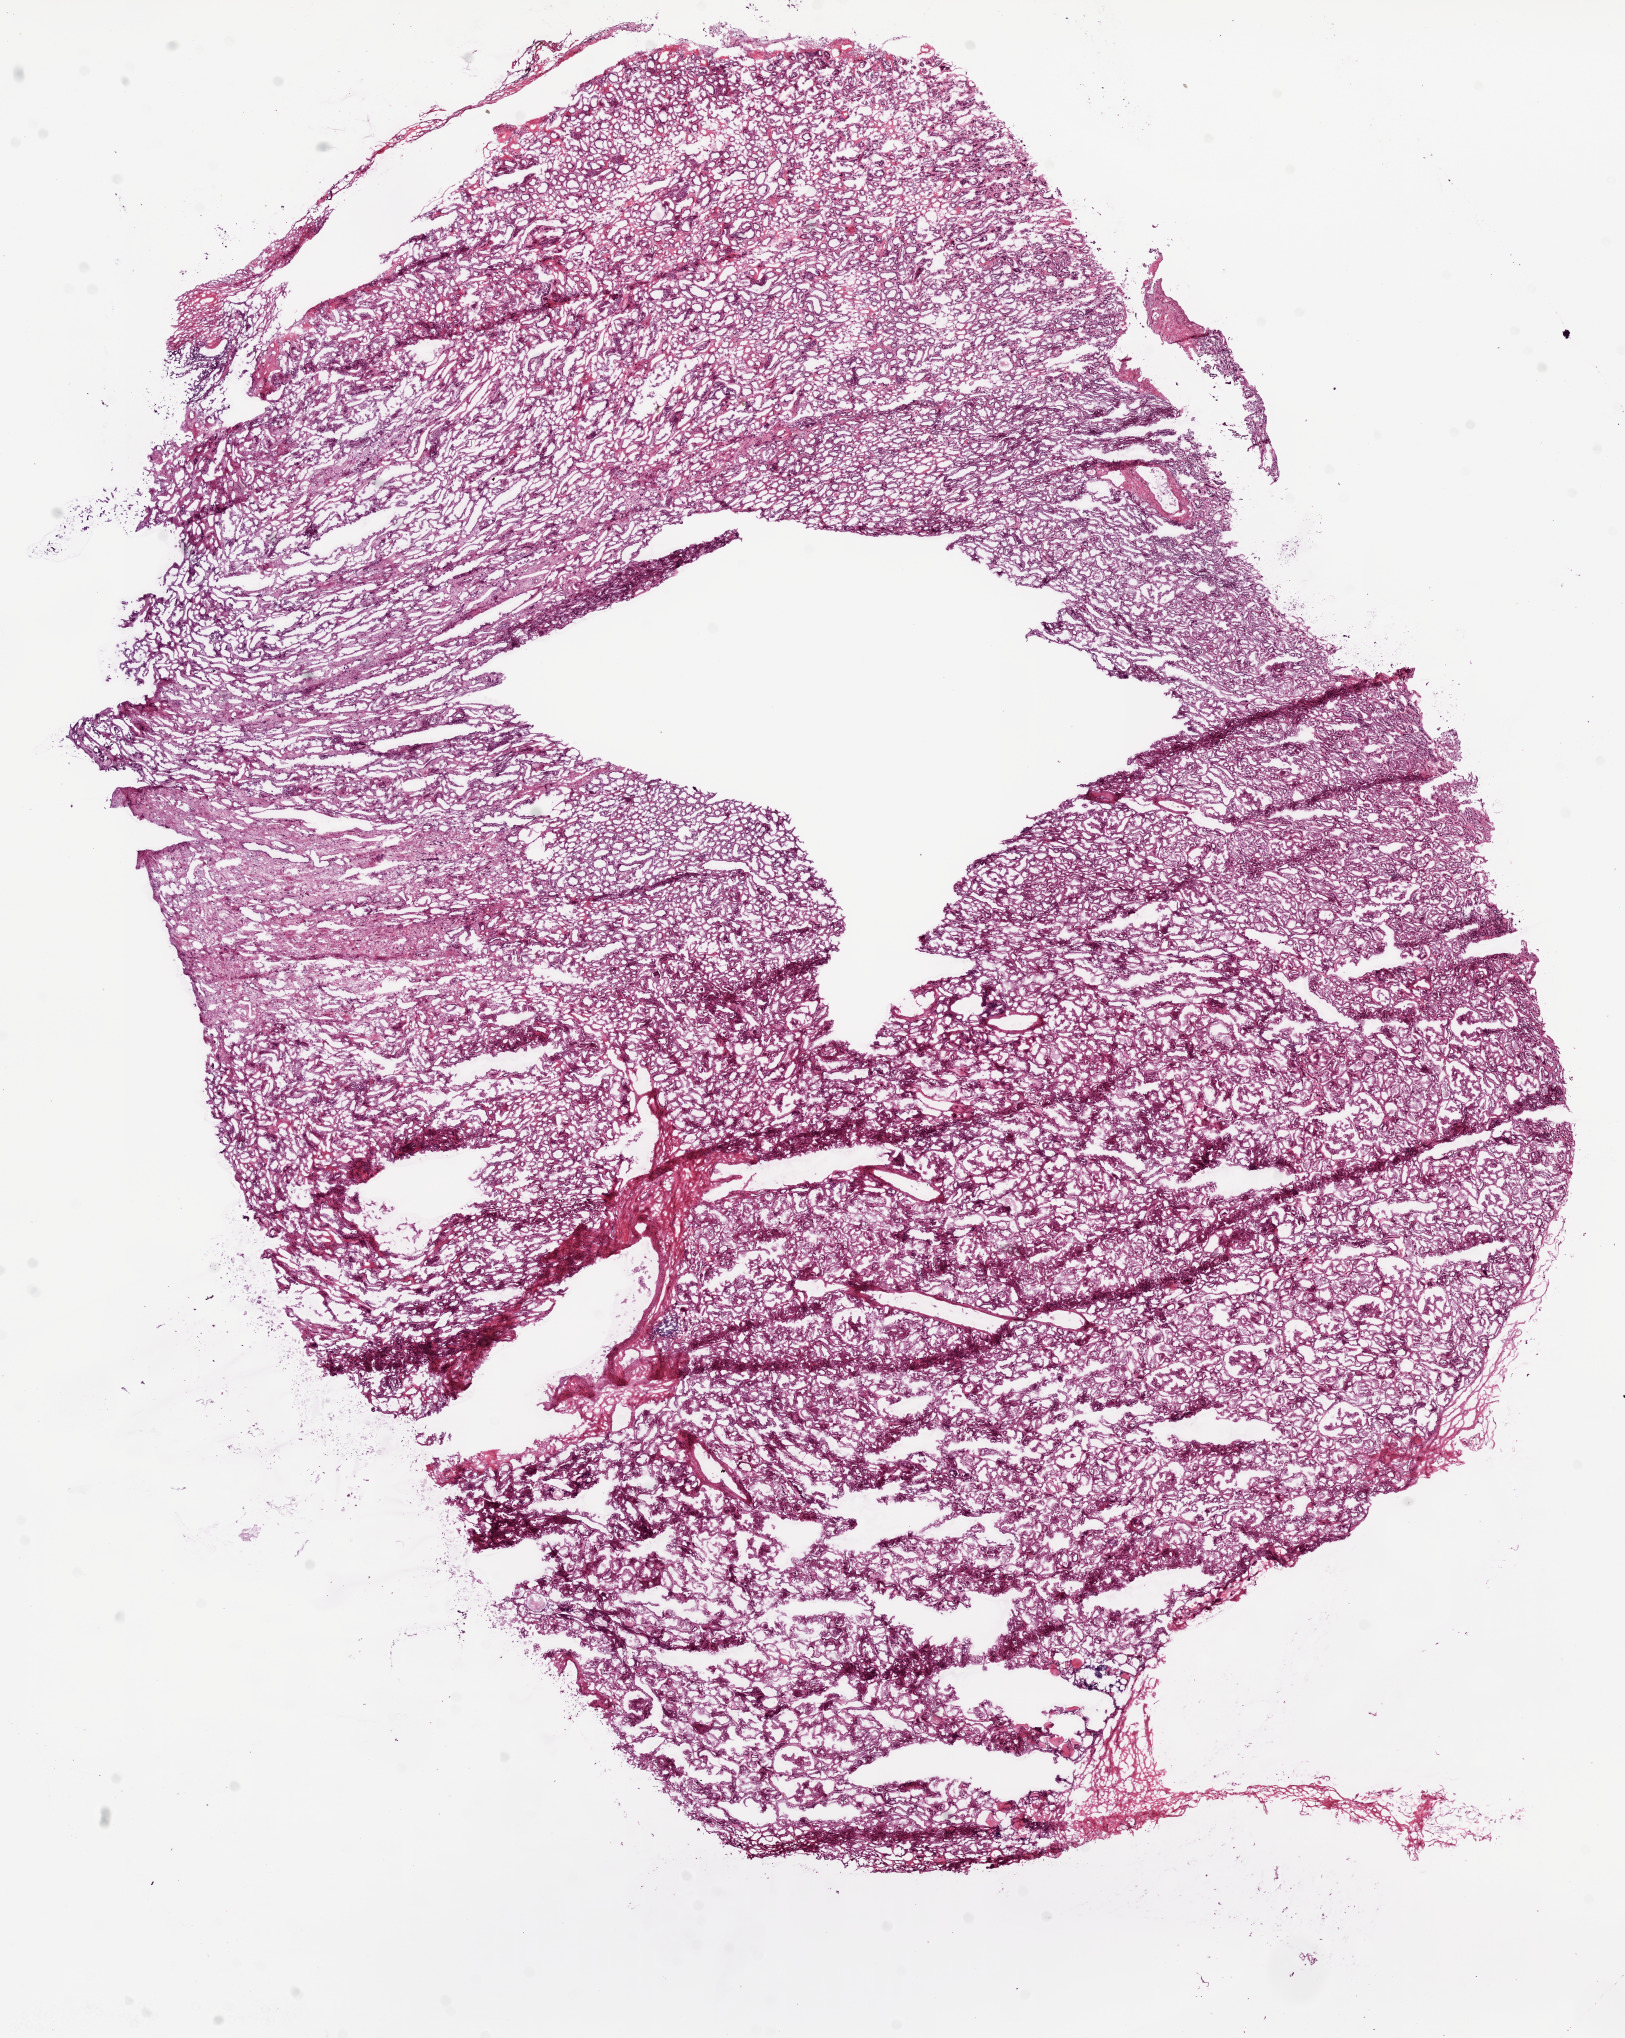
H&E whole-slide image, a low-resolution overview of the entire scanned area, about 13.0 x 16.4 mm (slide scanned at 20x), frozen section, kidney, solid tissue normal (non-tumour tissue) sample. Patient: male, age at initial diagnosis 65 years.
• this section: solid tissue normal sample (biorepository sample class)
• patient diagnosis: Clear cell adenocarcinoma, NOS